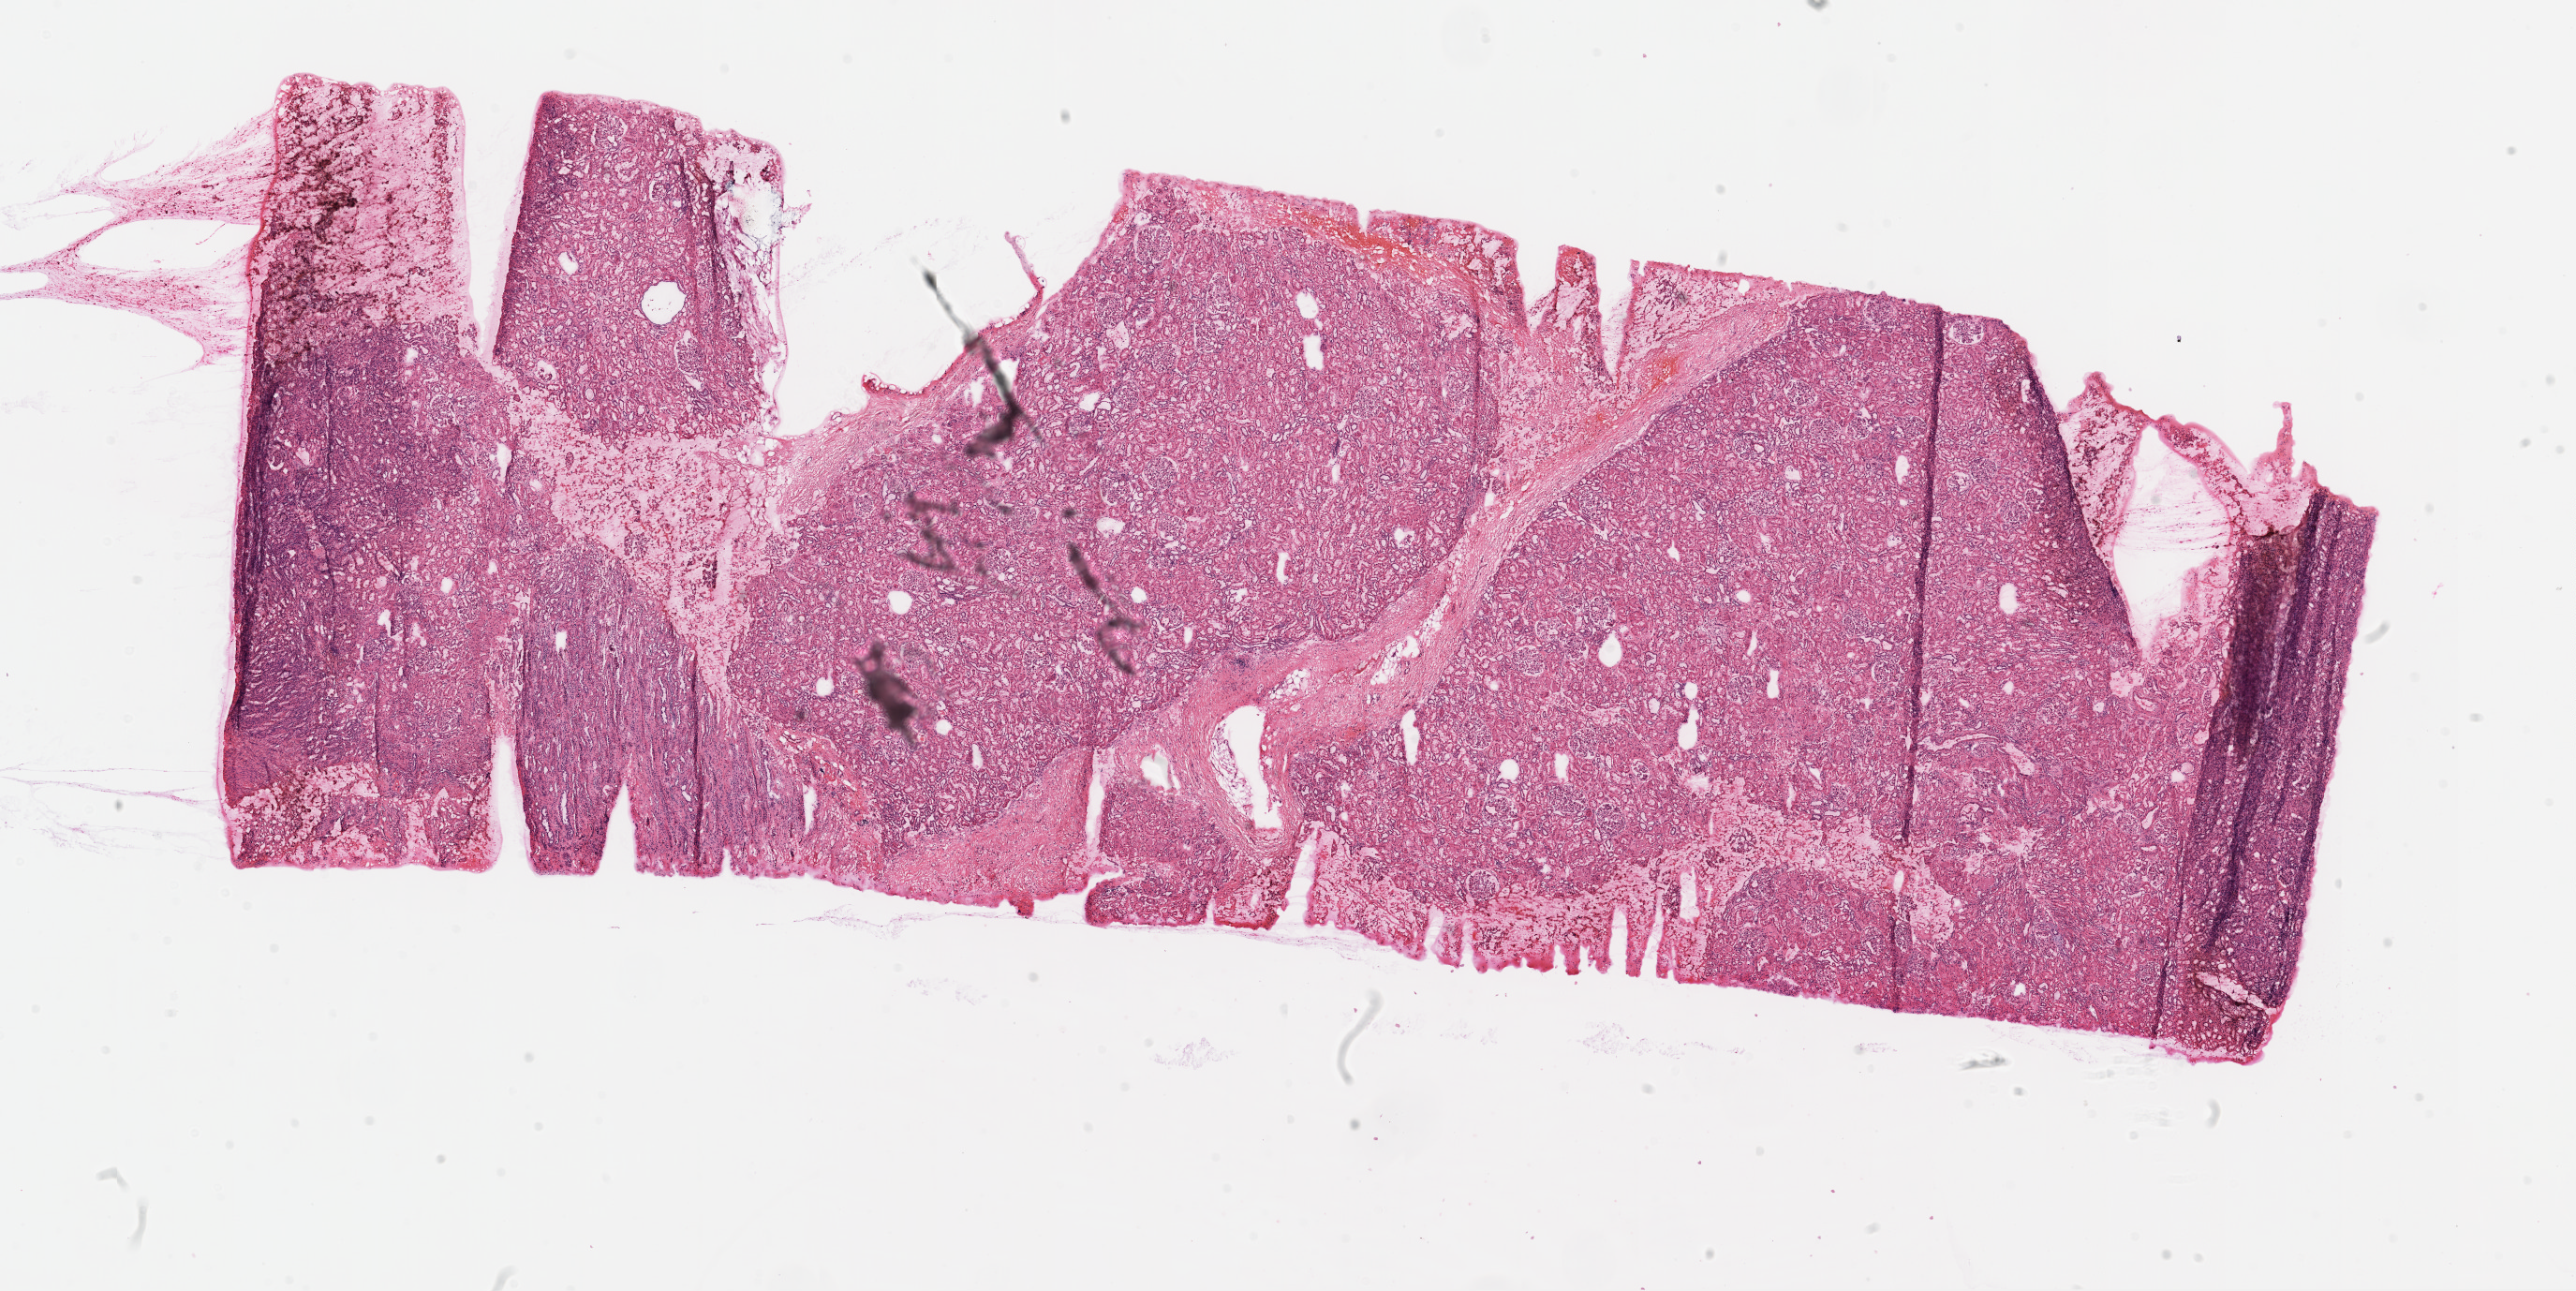
Whole-slide histology image, H&E-stained, whole scanned area (about 22.1 x 11.1 mm, slide scanned at 20x) shown as a low-resolution overview, frozen section, sample: solid tissue normal (non-tumour tissue), kidney. Female patient; age at initial diagnosis 52 years.
This section: solid tissue normal sample (biorepository sample class). Patient diagnosis: Clear cell adenocarcinoma, NOS.